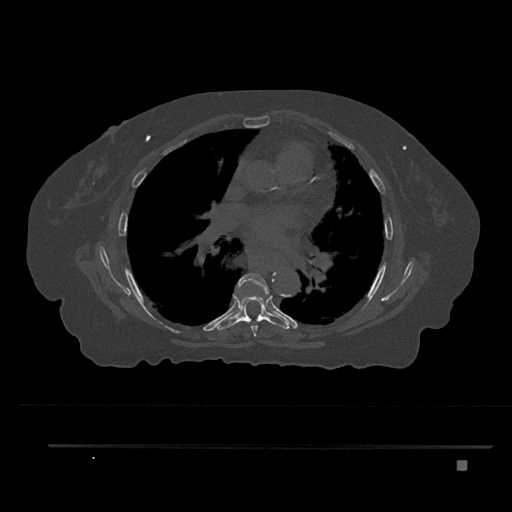
CT including the spine, one axial slice. Slice 502 of 797 in the series (ordered by position). Reconstruction kernel Br40s/3. 120 kVp. Bone window (W 1800 / L 400 HU). 512 × 512 image matrix, field of view 437 × 437 mm. Female patient, age 76 years. Case-level facts recorded for this patient, not image findings: primary cancer: lung.
Structures marked on this image (semi-automatically segmented with operator editing):
- T6 vertebra: bounding box [x1, y1, x2, y2] px = [236, 273, 269, 337]
- T7 vertebra: [217, 296, 290, 330]